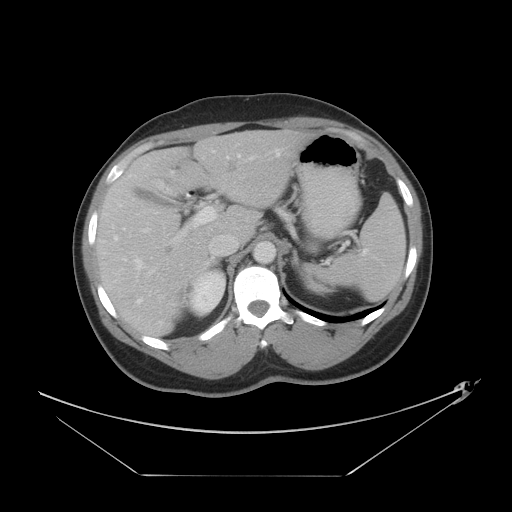
Contrast-enhanced abdominal CT, one axial slice. Position 27 of 44 along the scan axis. Reconstruction kernel STANDARD. Intravenous contrast given. Soft-tissue window (W 400 / L 40 HU). 5 mm slice thickness. 512 × 512 image matrix, field of view 466 × 466 mm. Male patient, age 49 years. Case-level facts recorded for this patient, not image findings: diagnosis: colorectal cancer liver metastases, imaged before liver resection; multiple liver metastases: no; largest metastasis: 8.5 cm.
Structures marked on this image (outlined manually by an expert reader):
- hepatic veins: box from (x=135, y=149) to (x=280, y=263) px
- liver: (x=96, y=130)–(x=315, y=338)
- planned liver remnant (the part of the liver to remain after resection): (x=126, y=131)–(x=315, y=242)
- portal vein (with intrahepatic branches): (x=114, y=161)–(x=247, y=269)
- liver metastasis: (x=224, y=160)–(x=238, y=174)